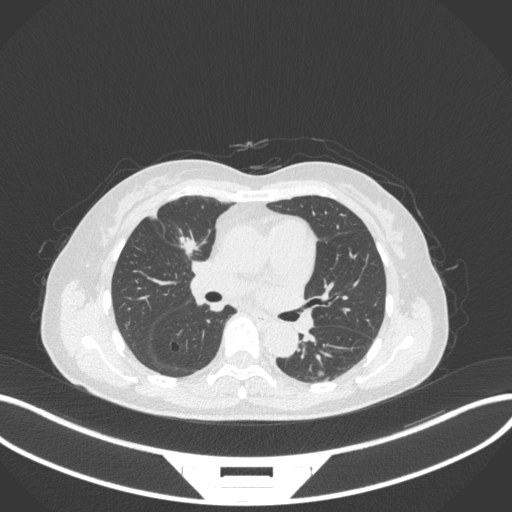
Chest CT, one axial slice; position 166 of 282 along the scan axis; reconstruction kernel B31f; 120 kVp; lung window (W 1500 / L -600 HU); 1 mm slice thickness; 512 × 512 image matrix, field of view 400 × 400 mm. Female patient, age 51 years. Case-level facts recorded for this patient, not image findings: clinical TNM (as recorded): T1c N0 M0.
Outlined on this slice (rectangle marked by the reading radiologist):
- lung tumour (recorded histology: adenocarcinoma): bounding box <177,232,205,260> (left, top, right, bottom; pixels)